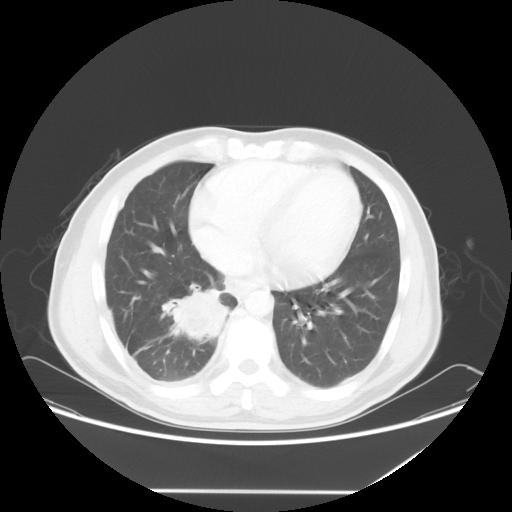
Chest CT, one axial slice. Position 23 of 60 along the scan axis. 120 kVp. Lung window (W 1500 / L -600 HU). 5 mm slice thickness. 512 × 512 image matrix, field of view 419 × 419 mm. Male patient, age 48 years. From the clinical record (not read from this slice): clinical TNM (as recorded): T3 N3 M1a.
Annotated regions visible in this slice (bounding box drawn by a radiologist):
- lung tumour (recorded histology: squamous cell carcinoma): bounding box [x1, y1, x2, y2] px = [162, 284, 233, 344]